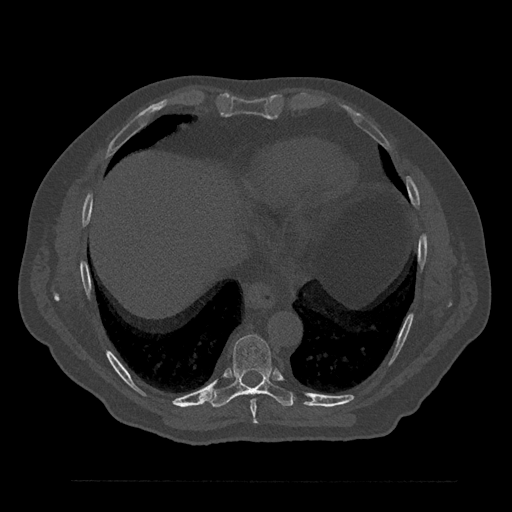
CT including the spine, one axial slice. Slice 416 of 797 in the series (ordered by position). Reconstruction kernel Br40s/3. Bone window (W 1800 / L 400 HU). 512 × 512 image matrix. Male patient, age 61 years. From the clinical record (not read from this slice): primary cancer: prostate.
Outlined on this slice (semi-automatic segmentation, software-assisted and operator-edited):
- T8 vertebra: bounding box (x1, y1, x2, y2) in pixels: (250, 399, 257, 424)
- T9 vertebra: (209, 335, 296, 408)